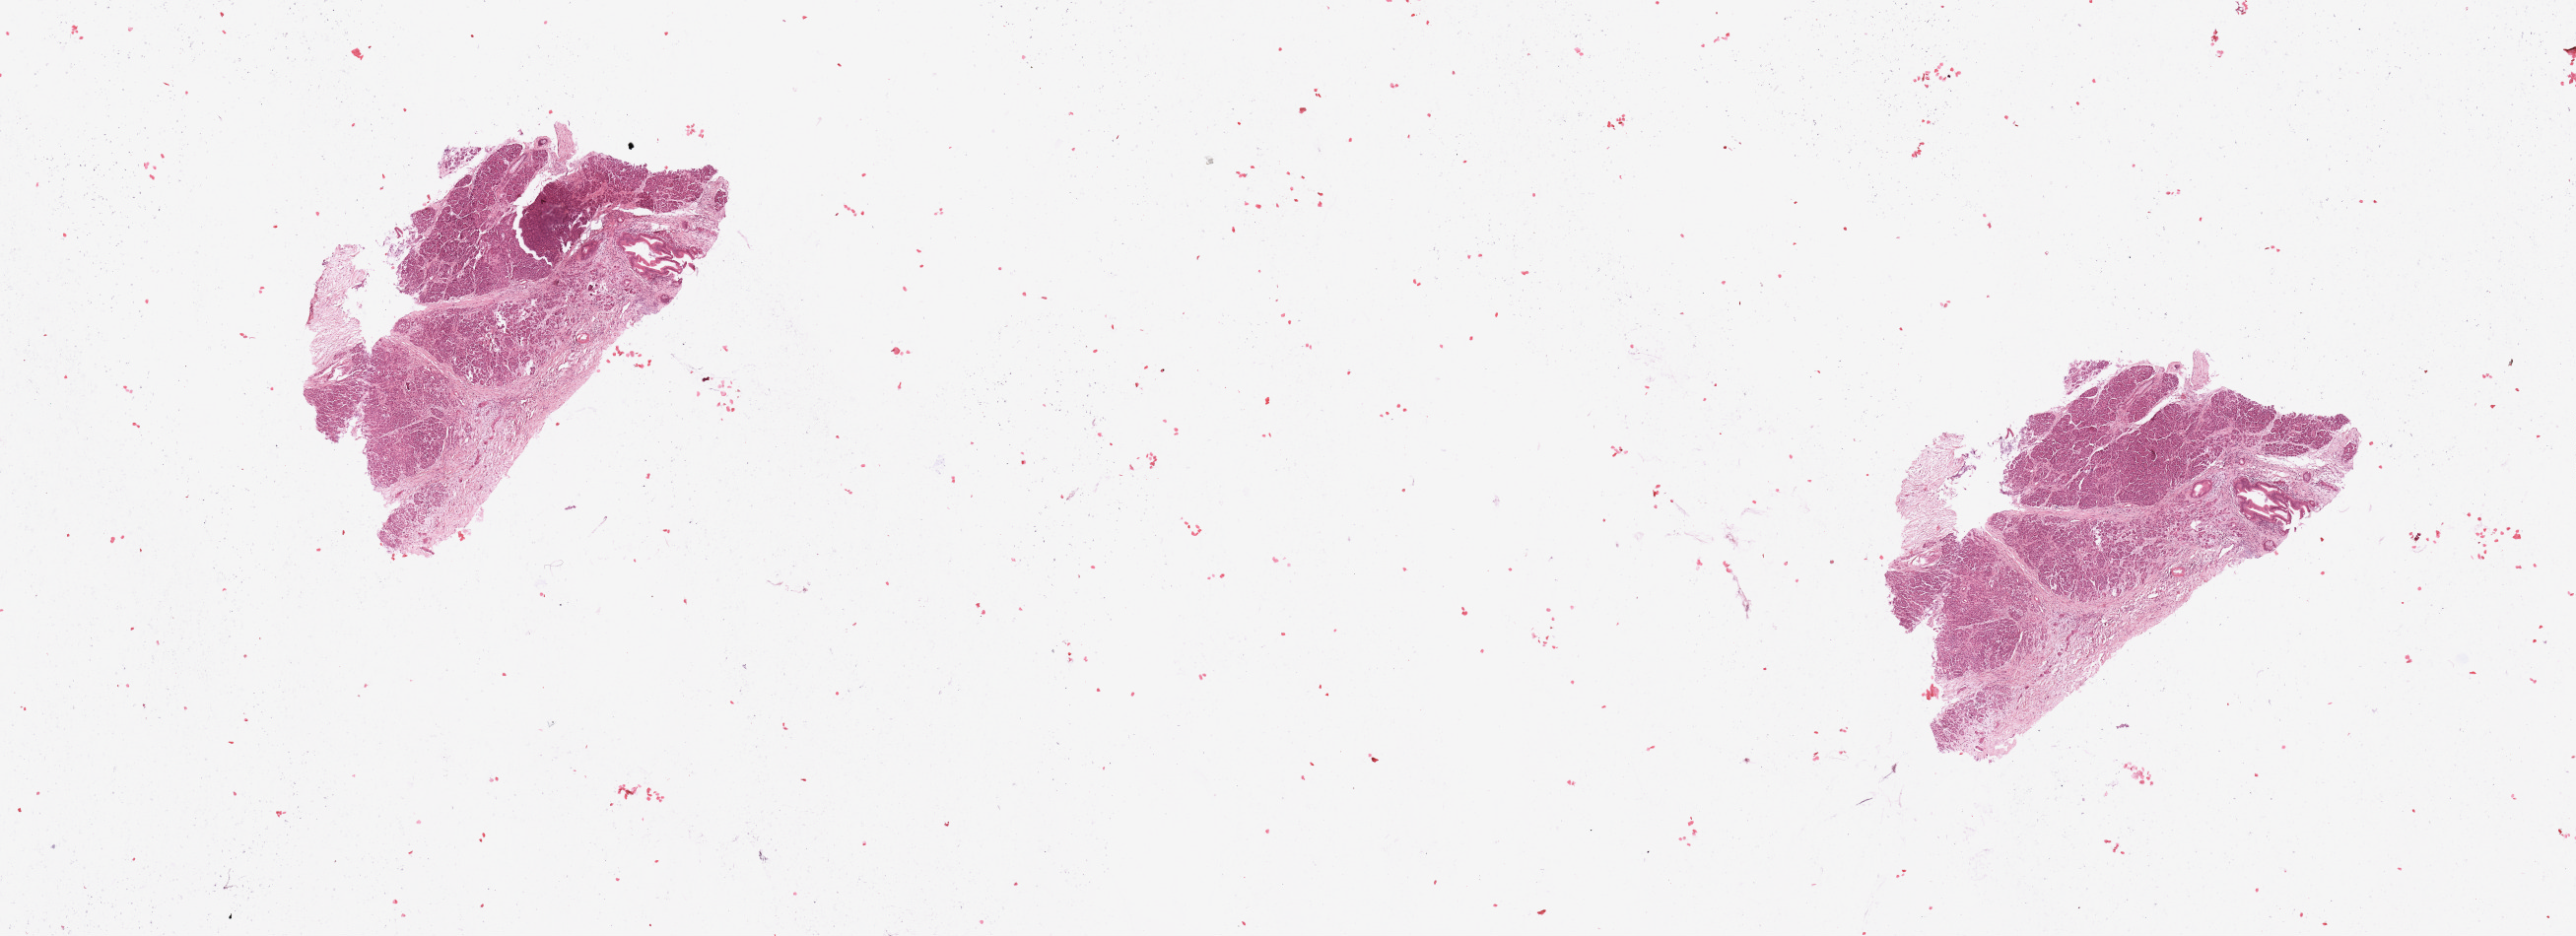
Digitized H&E tissue section (whole slide) — whole scanned area (about 20.7 x 7.5 mm, slide scanned at 20x) shown as a low-resolution overview, tumour tissue sample, sampled site: pancreas. 63-year-old male patient. Composition of this section per pathologist review: tumour nuclei 10%, necrosis 0%.
Histologic diagnosis: Infiltrating duct carcinoma, NOS.